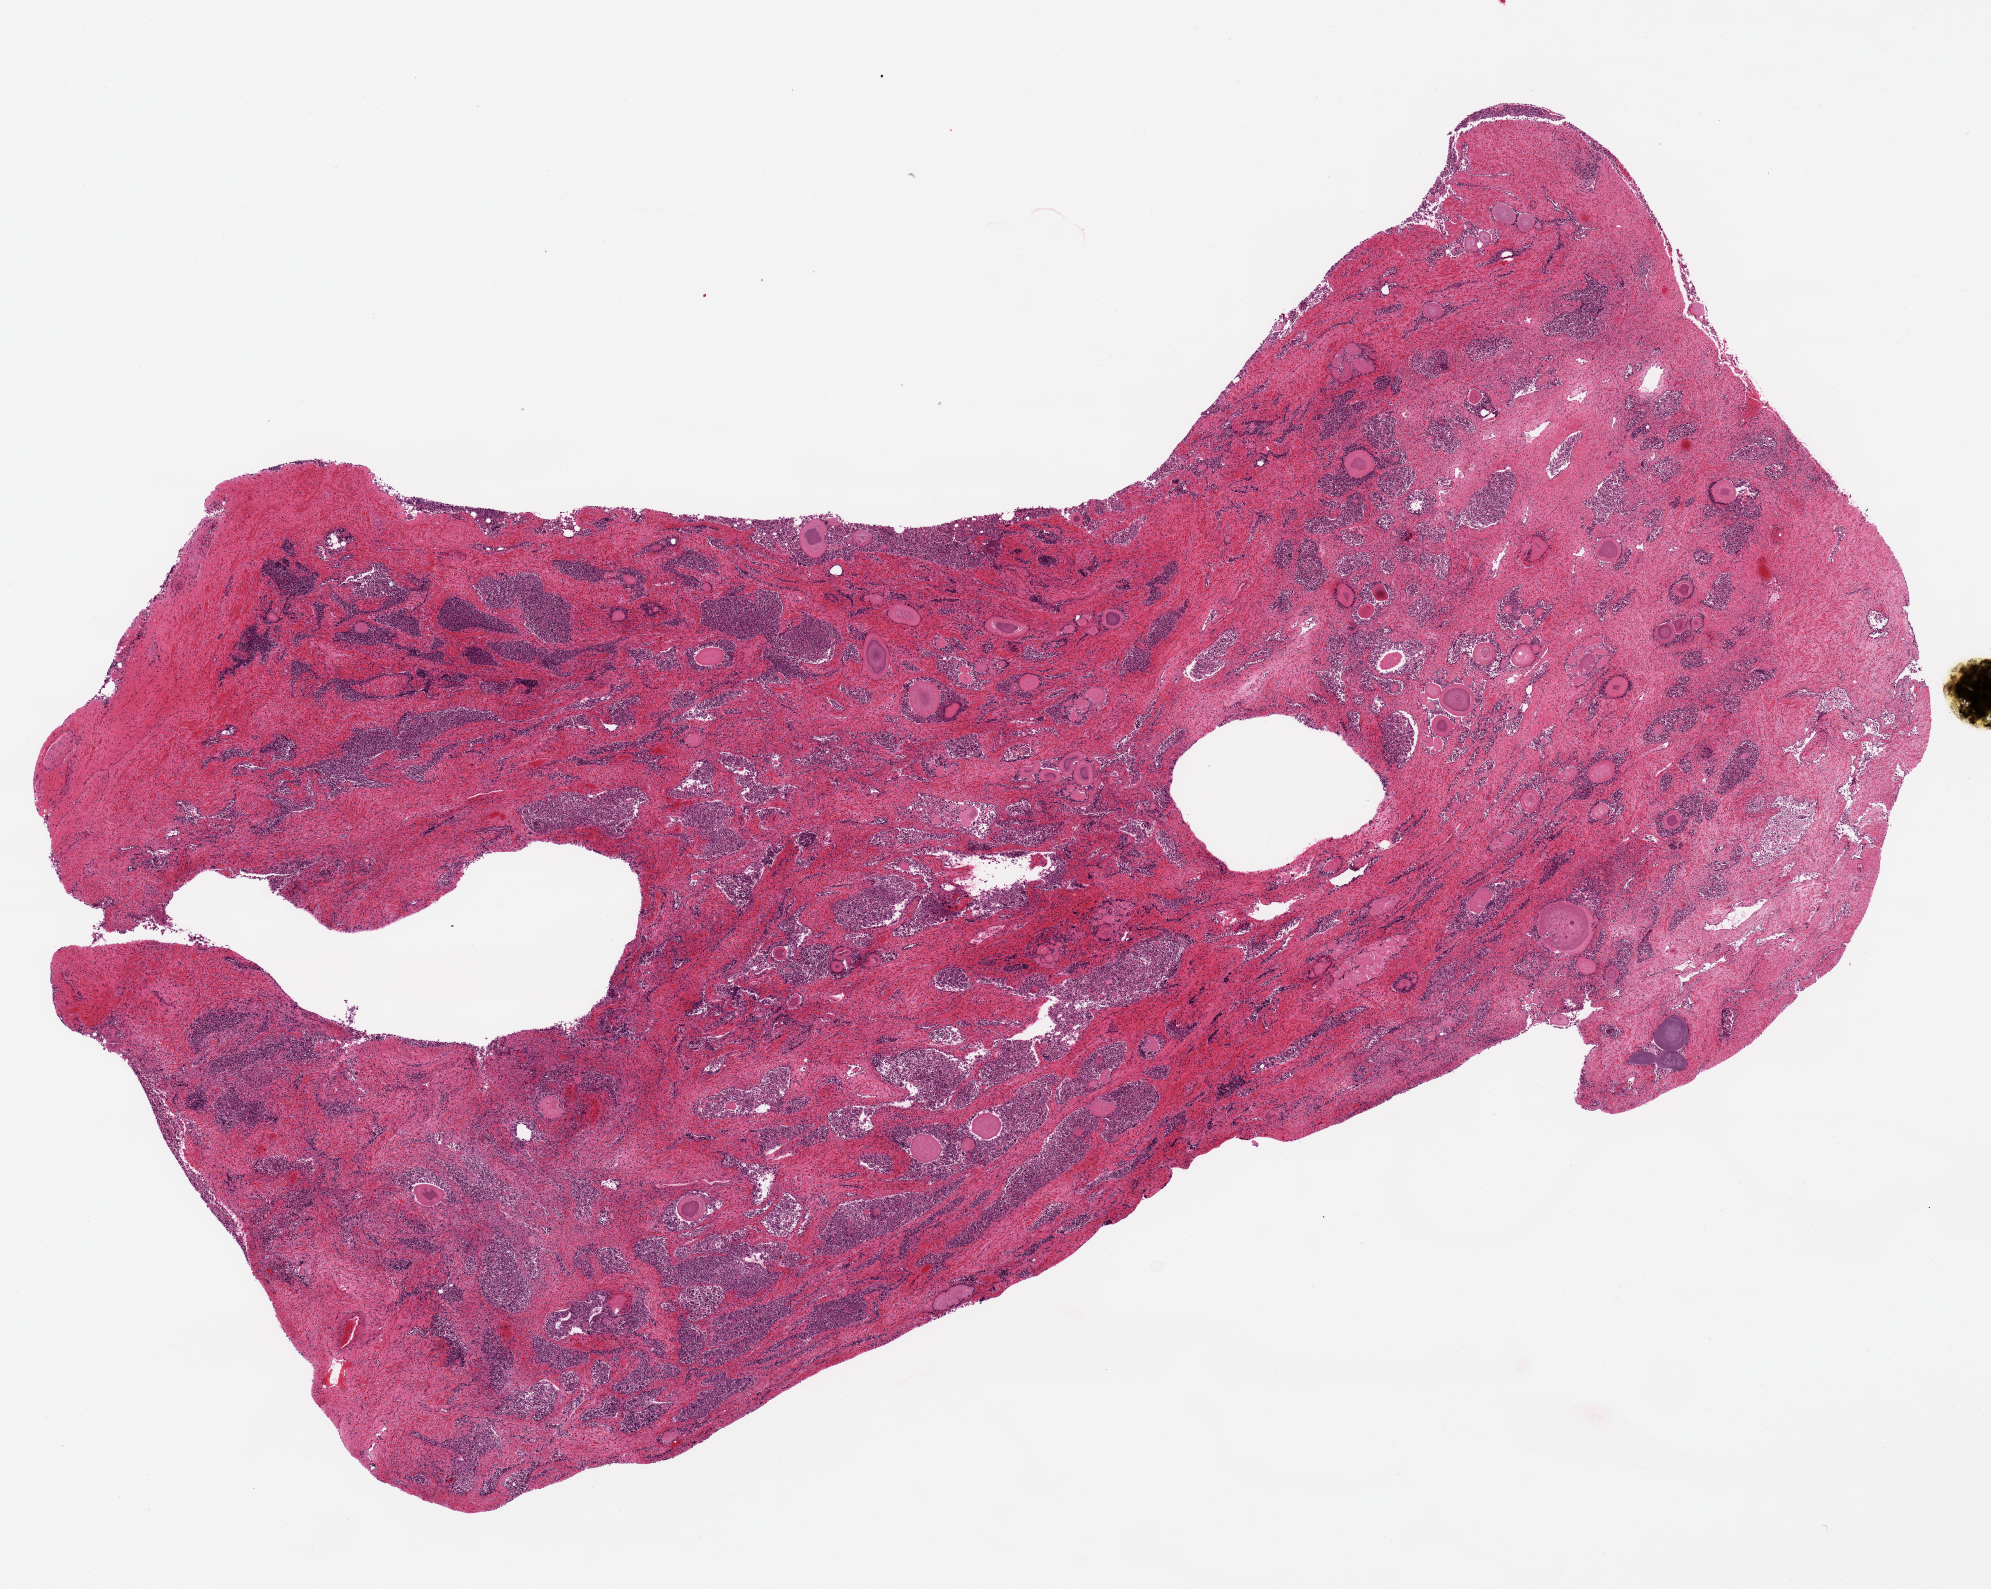
Digitized H&E-stained section, shown as a low-resolution overview of the whole scanned area (about 15.8 x 12.6 mm, from a 20x scan), PAXgene-fixed paraffin-embedded (PFPE) section, sampled site (target tissue): prostate, tissue donor sample. Donor: male.
- pathologist's review note for this sample: 15x8 mm aliquot